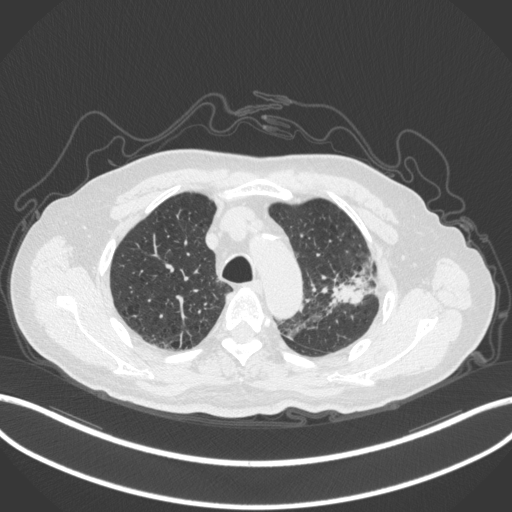
Chest CT, one axial slice; slice 230 of 331 in the series (ordered by position); reconstruction kernel B31f; 120 kVp; lung window (W 1500 / L -600 HU); 512 × 512 image matrix, field of view 400 × 400 mm. Patient: male, 79 years. Case-level facts recorded for this patient, not image findings: clinical TNM (as recorded): T2a N1 M1; histopathological grade: G3.
Structures marked on this image (rectangle marked by the reading radiologist):
- lung tumour (recorded histology: adenocarcinoma): bounding box <330,254,377,311> (left, top, right, bottom; pixels)